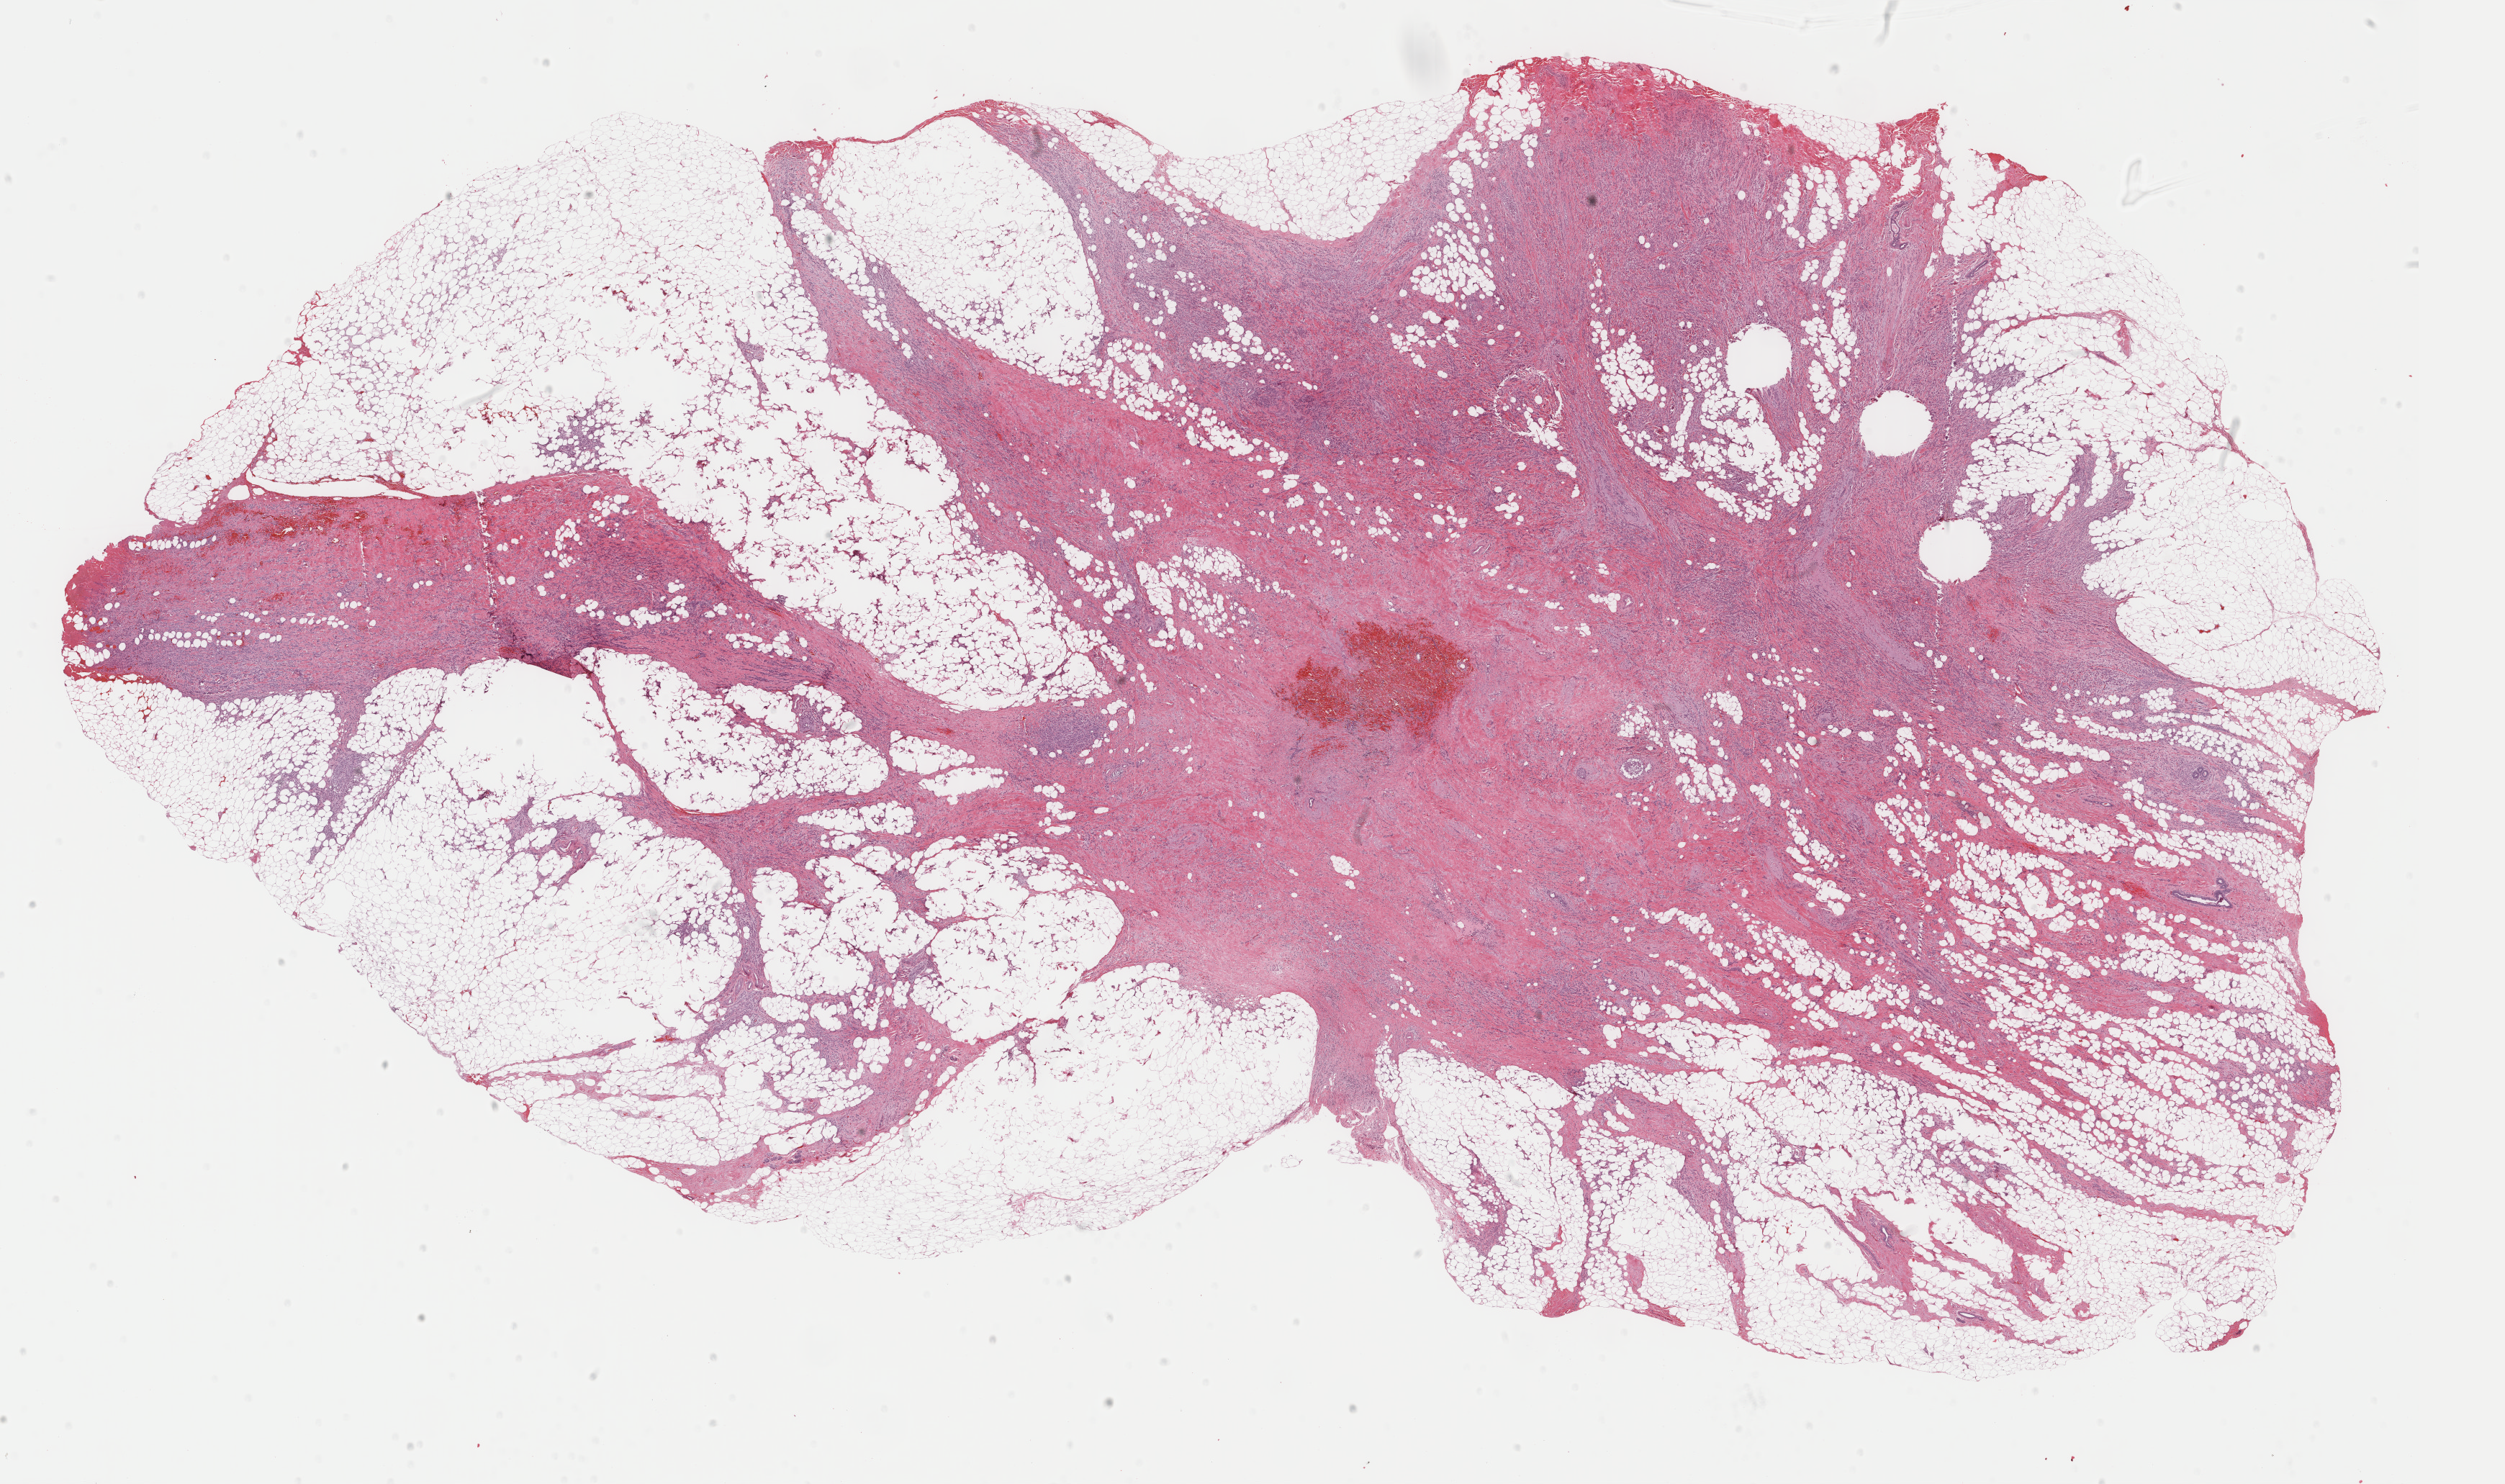
Whole-slide histology image, H&E — low-resolution overview of the scanned area, about 27.6 x 16.4 mm (slide scanned at 40x); FFPE section; sample: primary tumour, breast. Patient: female, age at initial diagnosis 62 years.
- diagnosis: Lobular carcinoma, NOS
- AJCC pathologic stage: IIA (6th edition)